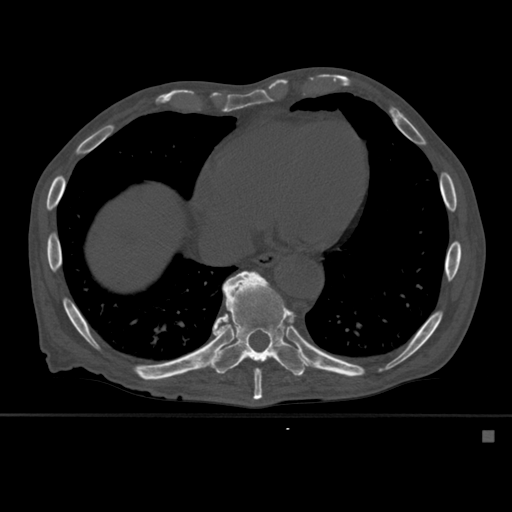
CT including the spine, one axial slice. Slice 321 of 527 in the series (ordered by position). Bone window (W 1800 / L 400 HU). 512 × 512 image matrix, field of view 373 × 373 mm. Patient: male, 78 years. Case-level facts recorded for this patient, not image findings: primary cancer: prostate.
Structures marked on this image (semi-automatically segmented with operator editing):
- T10 vertebra: box from (x=210, y=271) to (x=308, y=377) px
- T9 vertebra: (x=227, y=271)–(x=291, y=400)